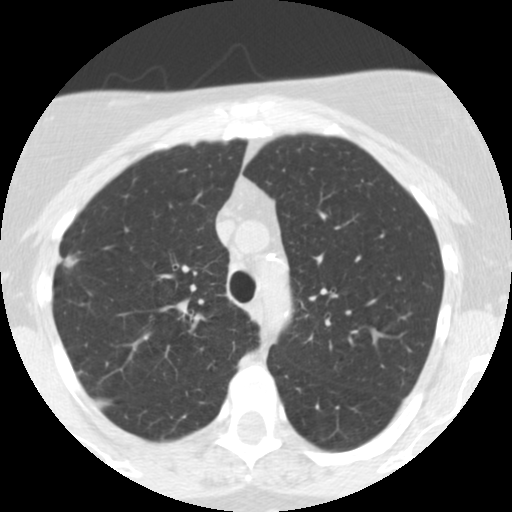
Low-dose screening chest CT, one axial slice; position 184 of 248 along the scan axis; reconstruction kernel STANDARD; 120 kVp; lung window (W 1500 / L -600 HU); 512 × 512 image matrix, field of view 287 × 287 mm.
Outlined on this slice (outlined manually by an expert reader):
- lesion 1 (tumor, upper lobe of right lung): bounding box (x1, y1, x2, y2) in pixels: (64, 256, 78, 268)